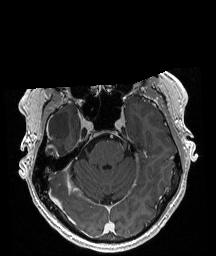
Brain MRI from a brain-tumour surgery series, one axial slice. Slice 136 of 208 in the series (ordered by position). T1-weighted post-contrast. 216 × 256 image matrix, field of view 211 × 250 mm. Case-level facts recorded for this patient, not image findings: histopathology: Astrocytoma; WHO grade: 4; IDH mutation: yes.
Annotated regions visible in this slice (outlined manually by an expert reader):
- tumour: bounding box <45,144,59,171> (left, top, right, bottom; pixels)